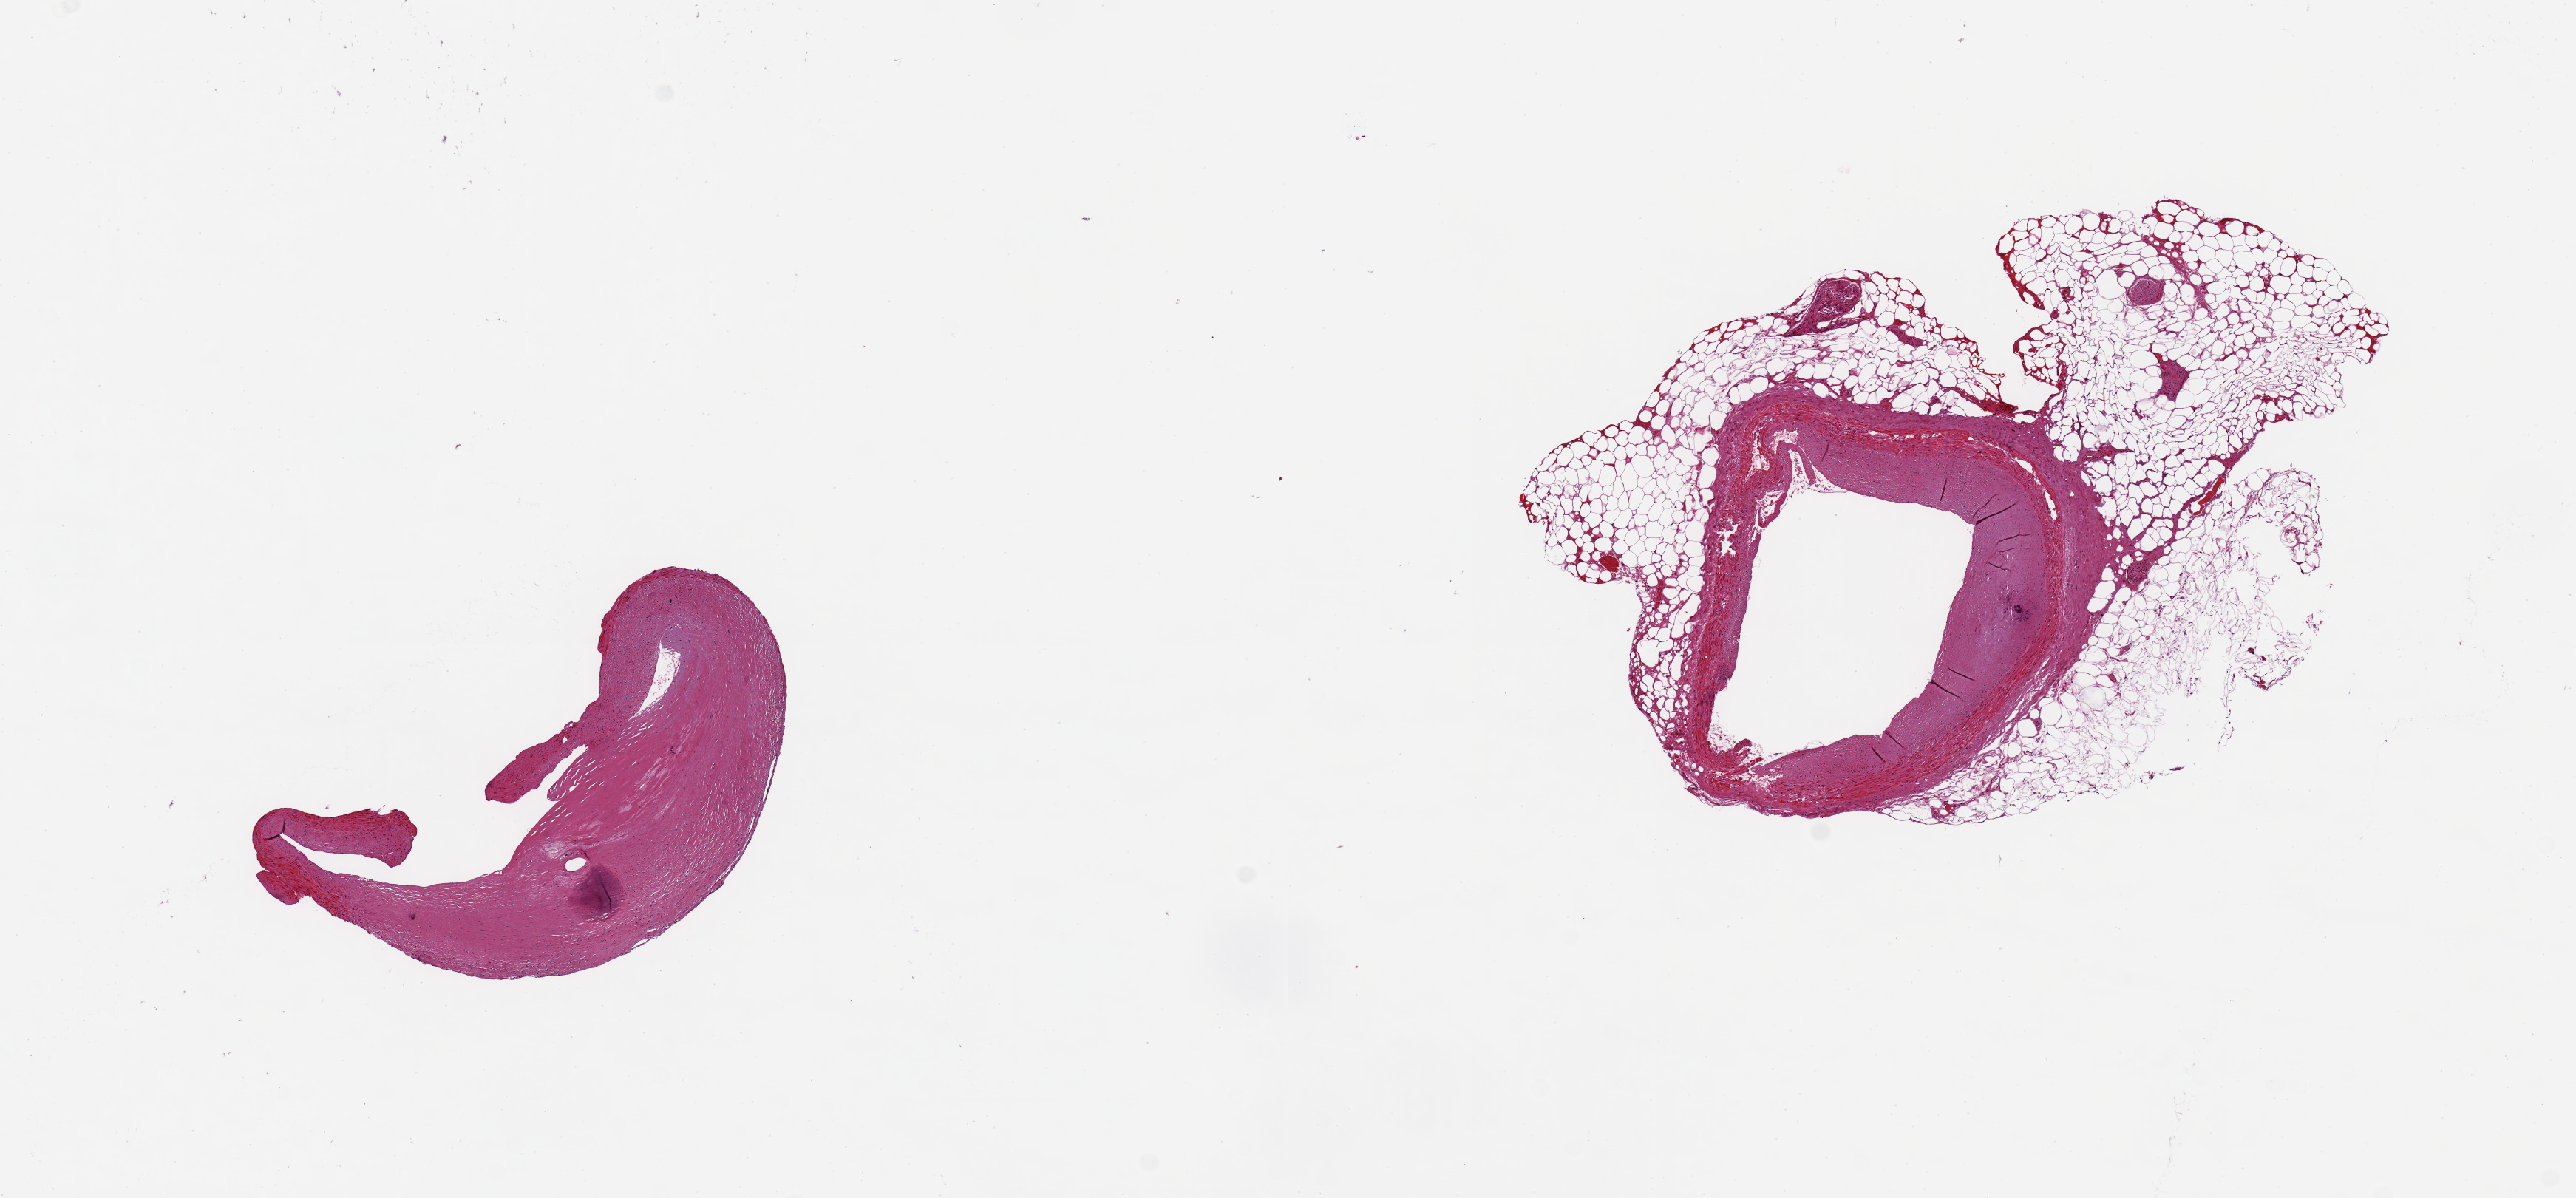
Digitized H&E-stained section, brightfield — whole scanned area (about 13.8 x 6.4 mm) shown as a low-resolution overview. Donor: male.
Specimen: PAXgene-fixed paraffin-embedded (PFPE) section; target tissue: coronary artery; tissue donor sample.